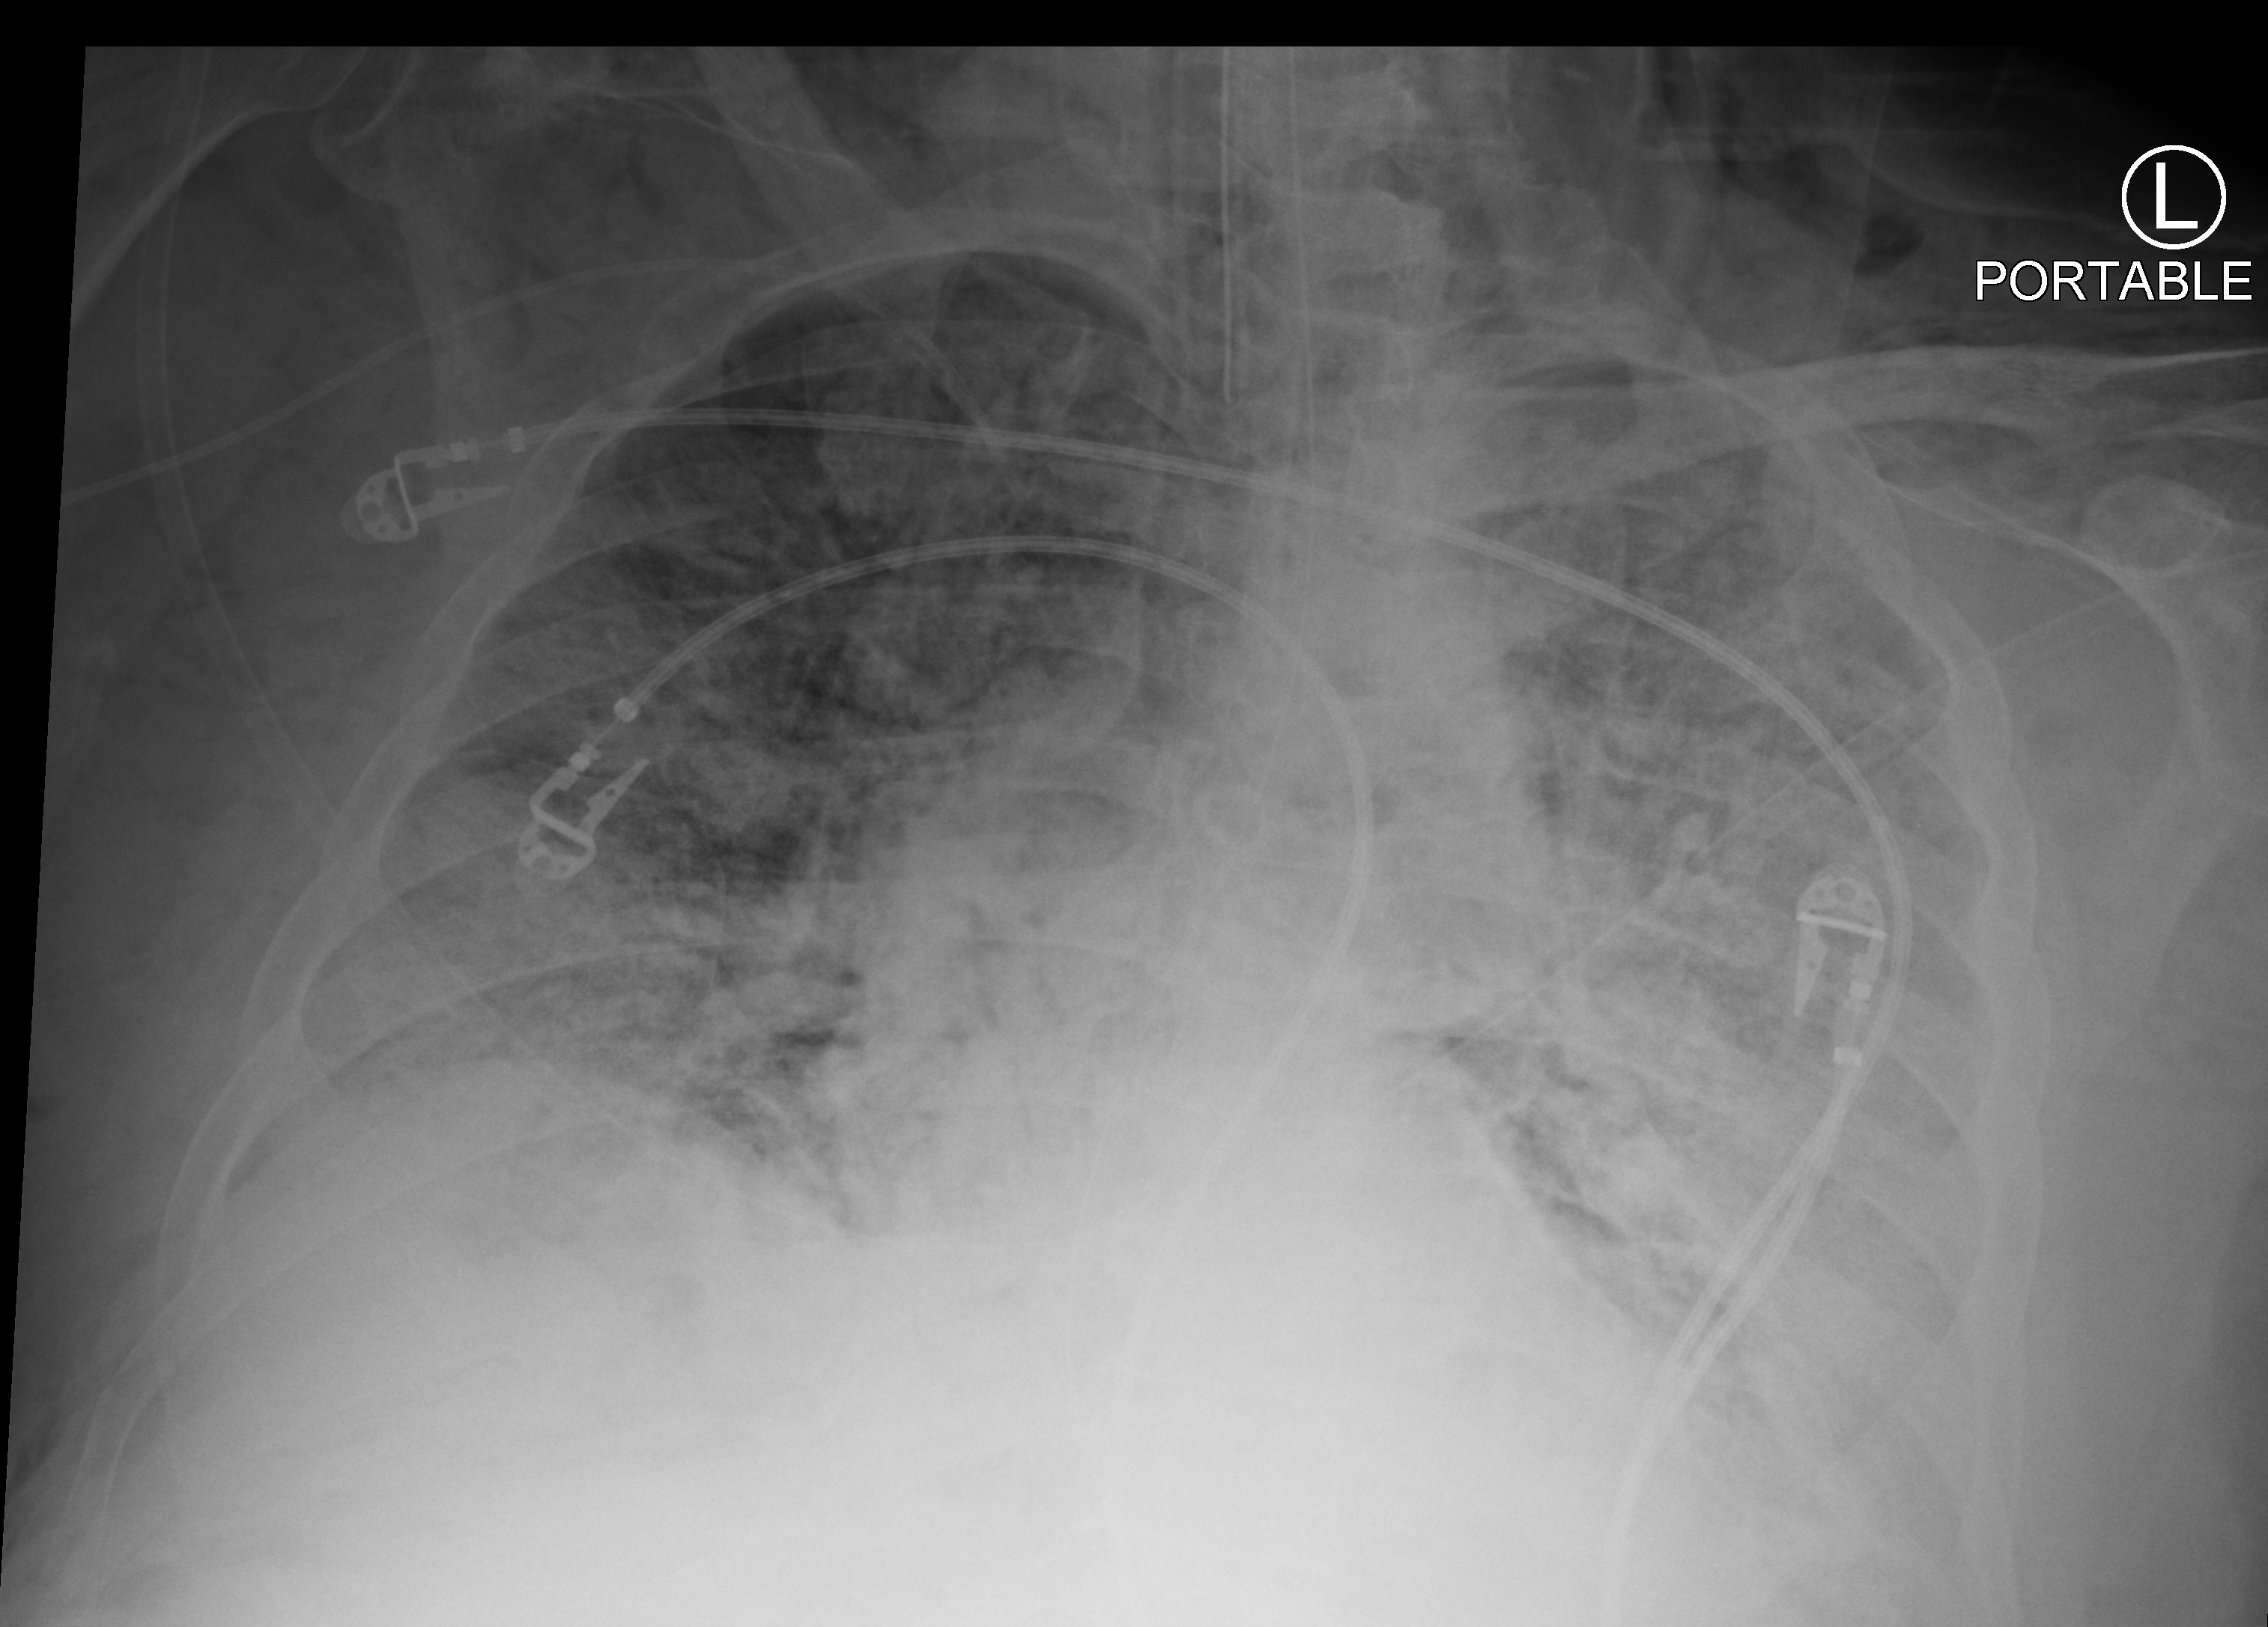
Bedside chest radiograph (computed radiography), anteroposterior (AP) projection. Adult patient hospitalised with COVID-19, age 18–59 years.
Admission-level facts for this patient (not findings on this image; timing relative to this image not recorded): admitted to intensive care during this hospital stay: yes; smoking status (admission record): never; mechanically ventilated during this hospital stay: yes.